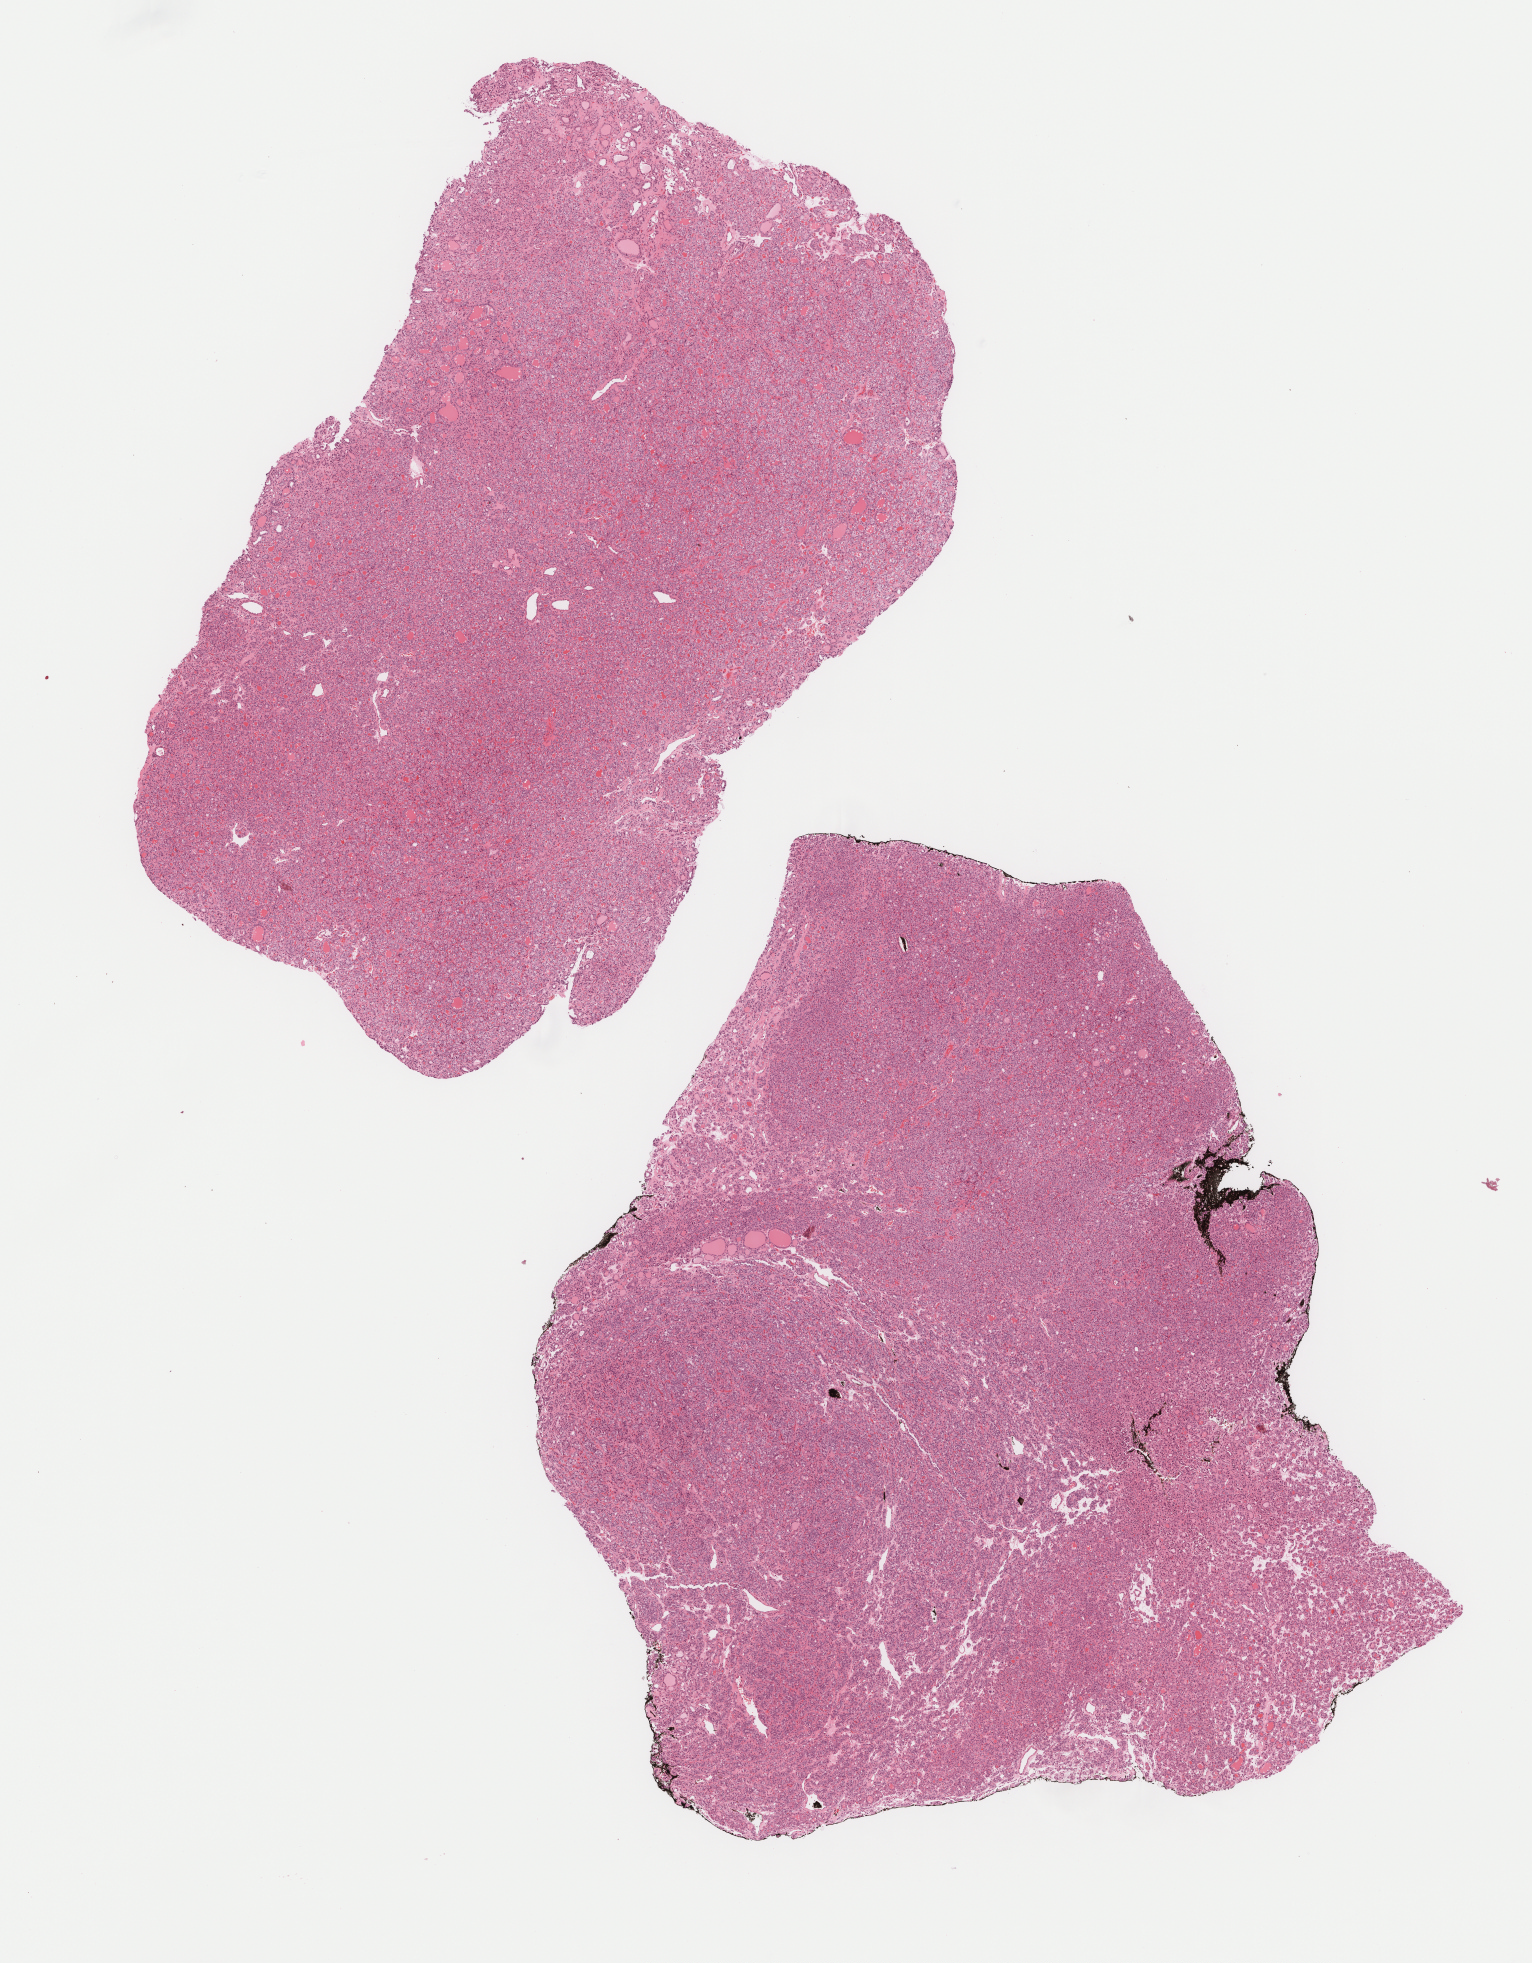
H&E-stained whole-slide image — whole scanned area (about 12.3 x 15.8 mm, acquisition: 40x scan) shown as a low-resolution overview. Formalin-fixed paraffin-embedded (FFPE) diagnostic section. Thyroid, primary tumour sample. Male, age 36 years at initial diagnosis.
Diagnosis: Papillary carcinoma, follicular variant (thyroid gland).